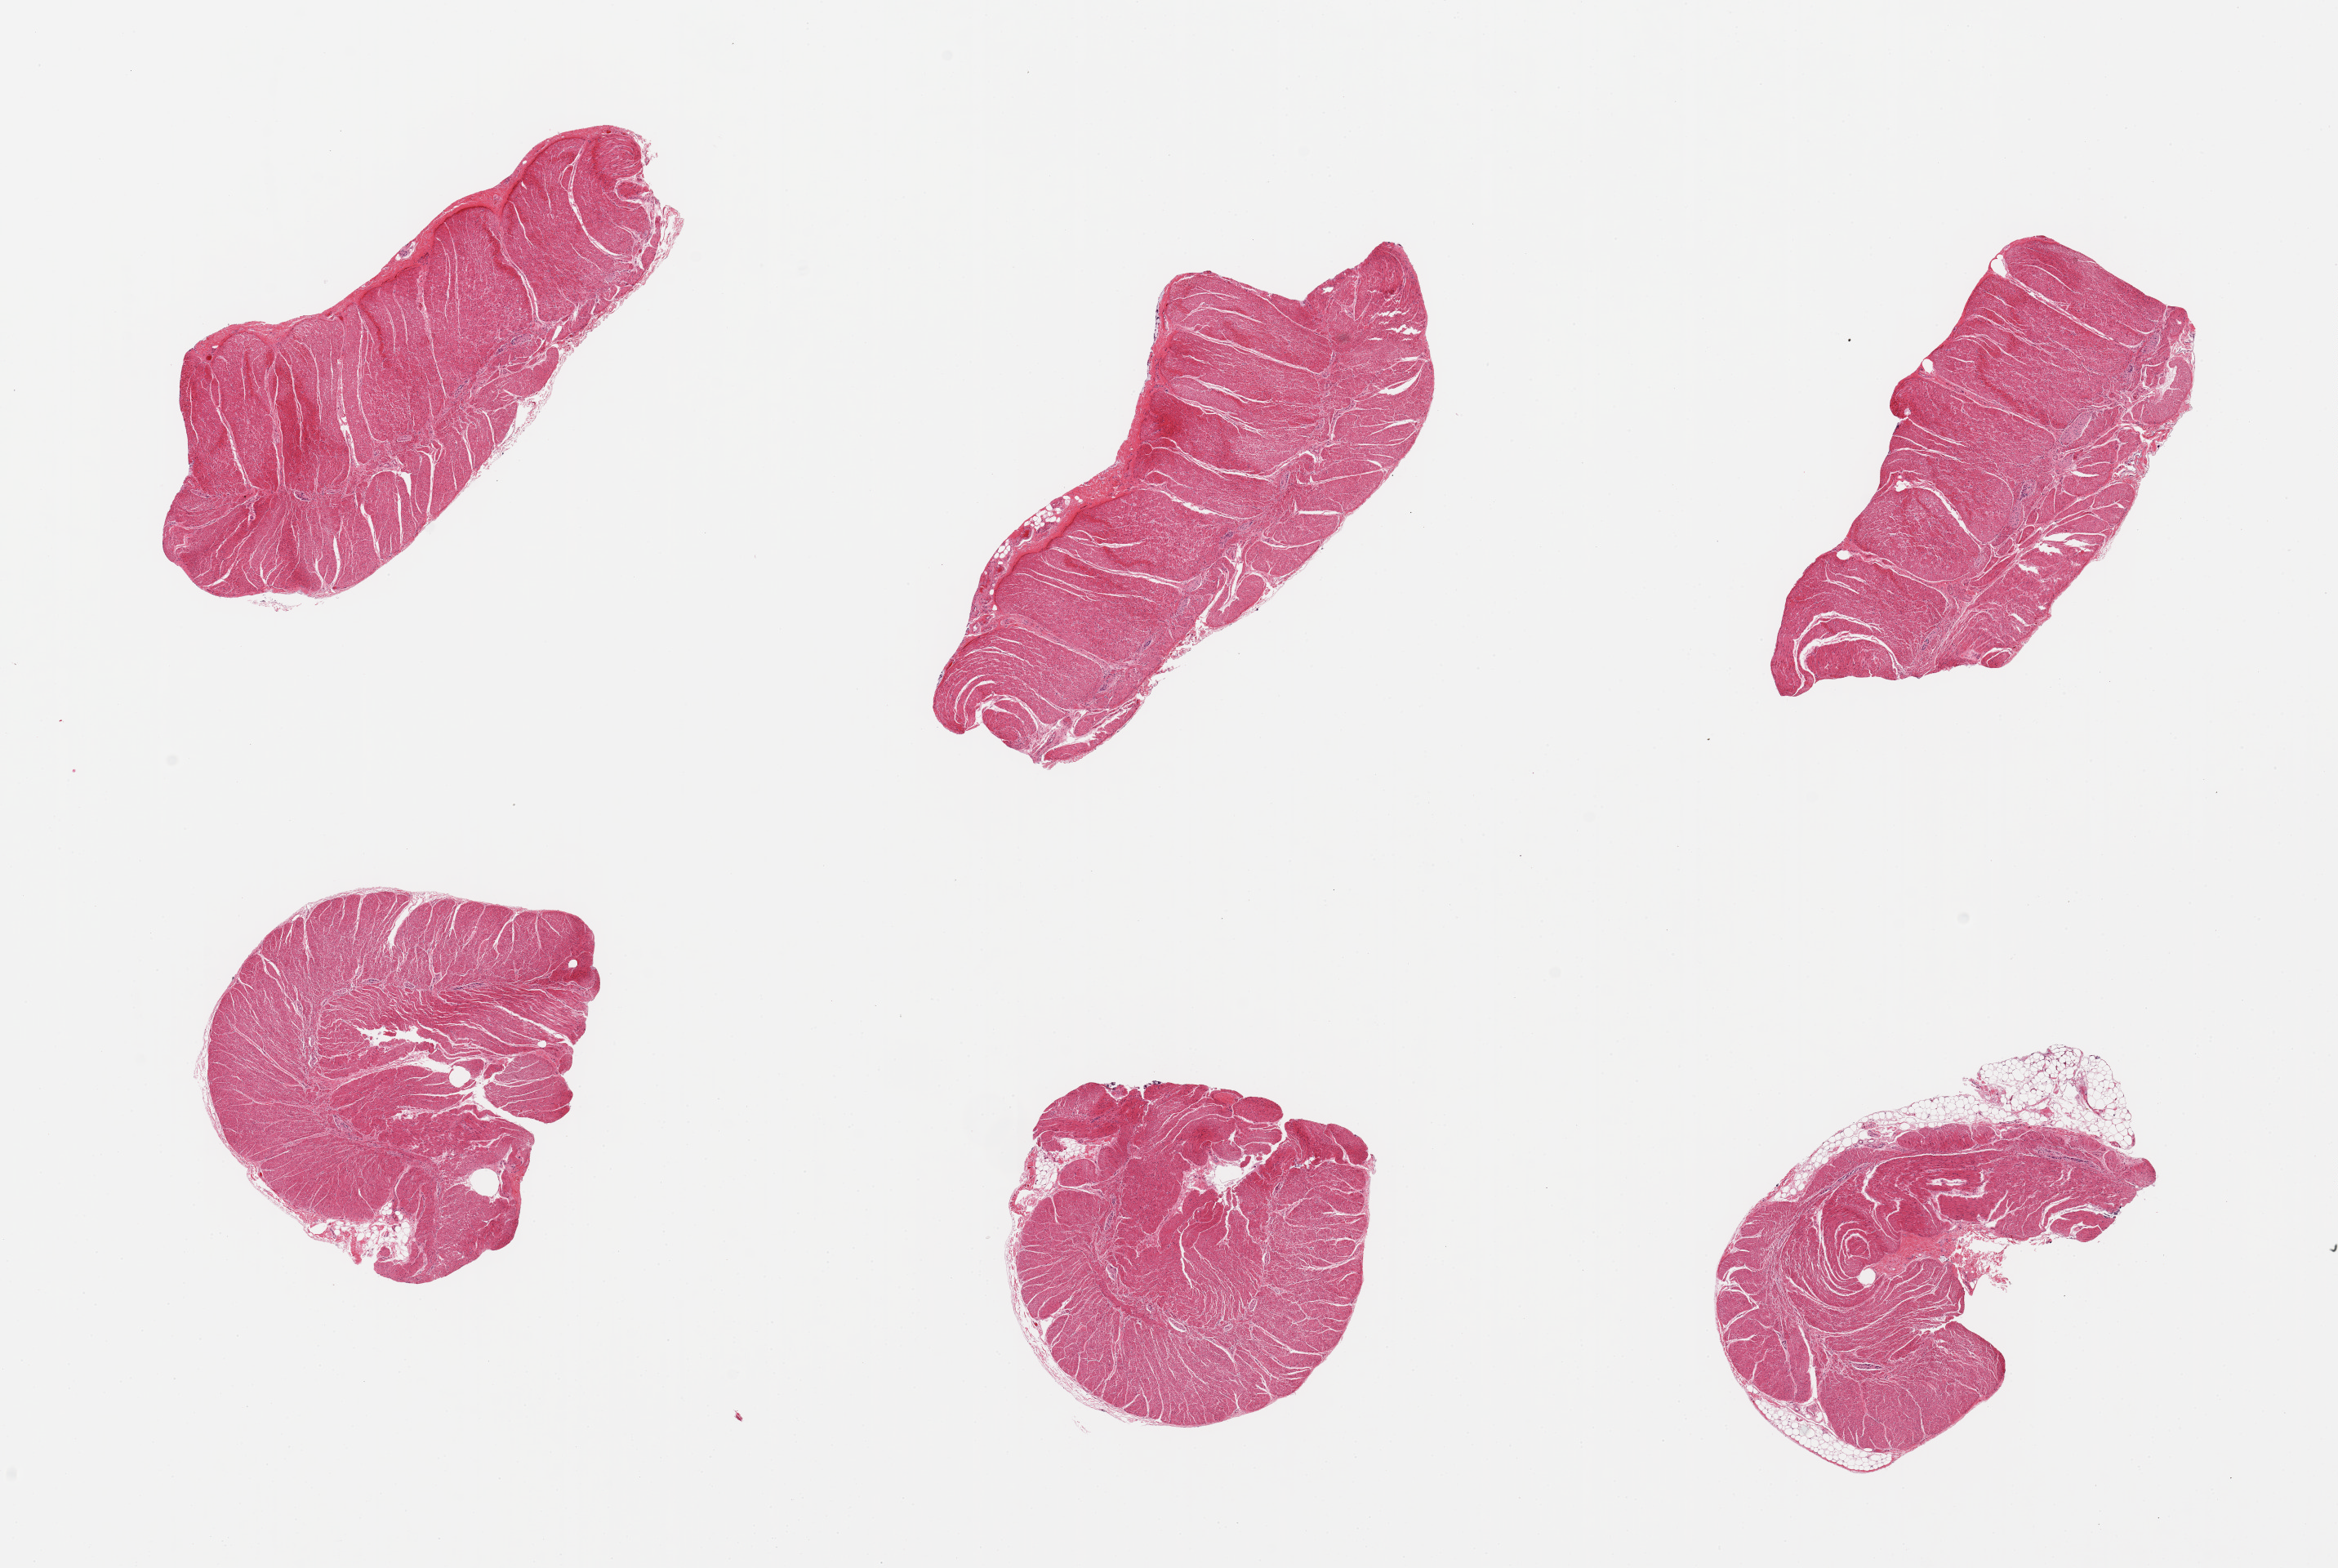
Hematoxylin and eosin (H&E) whole-slide image, brightfield — shown as a low-resolution overview of the whole scanned area (about 22.6 x 15.2 mm); PAXgene-fixed, paraffin-embedded tissue; target tissue: sigmoid colon; tissue donor sample. Donor sex: male.
Review note (as recorded): 6 pieces; predominantly well trimmed, but one piece has ~15% fat attached.